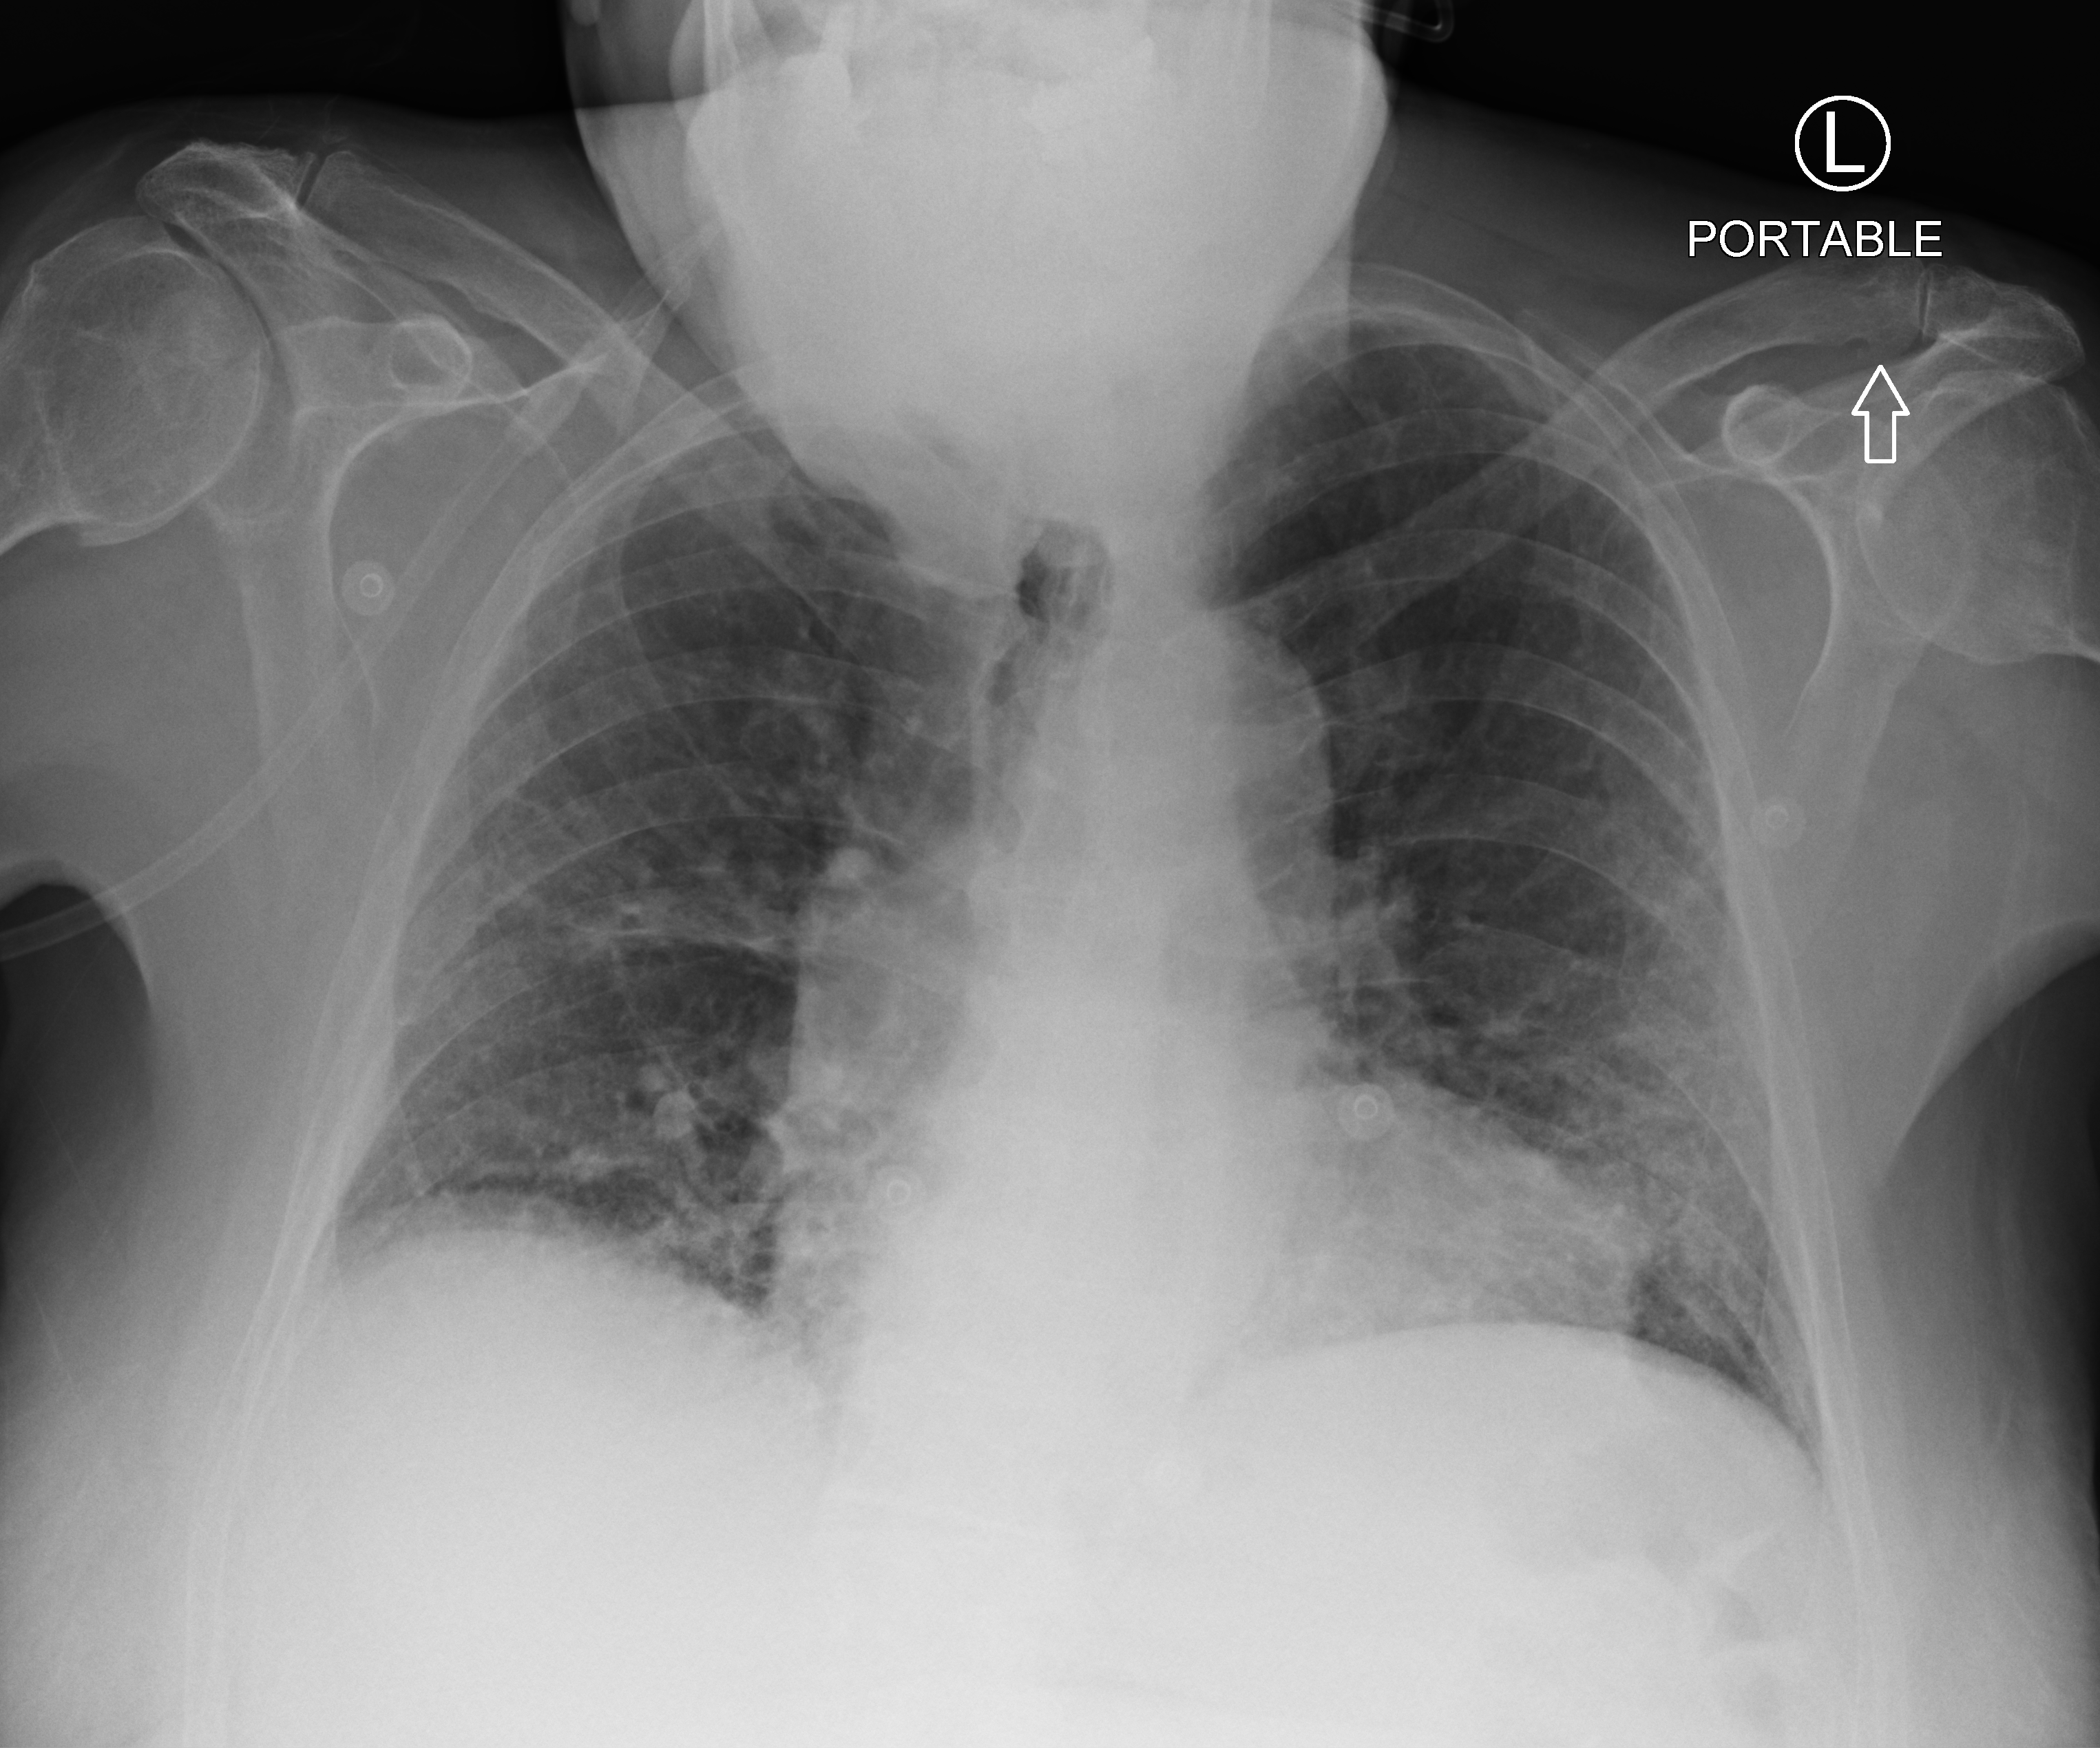
Bedside chest radiograph (computed radiography), anteroposterior (AP) projection. Male patient hospitalised with COVID-19, age 75–90 years.
Admission-level facts for this patient (not findings on this image; timing relative to this image not recorded): mechanically ventilated during this hospital stay: no.